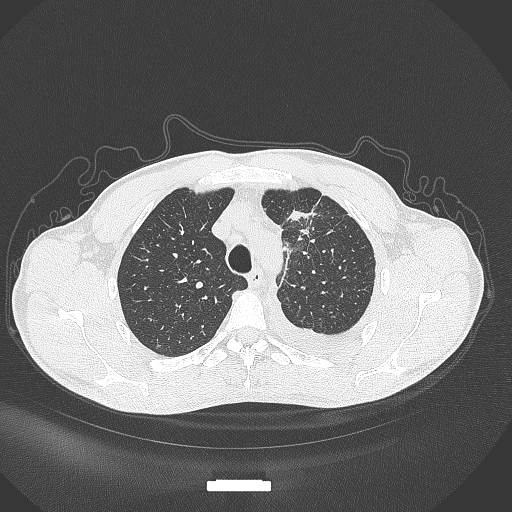
Chest CT, one axial slice. Reconstruction kernel B70f. Lung window (W 1500 / L -600 HU). 1 mm slice thickness. 512 × 512 image matrix. Patient: male, 49 years. Case-level facts recorded for this patient, not image findings: clinical TNM (as recorded): T1c N1 M1.
Outlined on this slice (bounding box drawn by a radiologist):
- lung tumour (recorded histology: adenocarcinoma): bounding box [x1, y1, x2, y2] px = [281, 205, 323, 230]